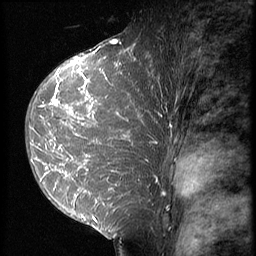
Breast MRI (dynamic contrast-enhanced), one sagittal slice; slice 39 of 64 in the series (ordered by position); 3 images stored at this slice position (order not interpretable as contrast timing); 1.5 T; TE 4.2 ms, TR 9 ms; 256 × 256 image matrix, field of view 180 × 180 mm. Female patient, age 39 years. From the clinical record (not read from this slice): setting: breast cancer imaged before/during neoadjuvant chemotherapy; receptor status: HER2-positive.
Annotated regions visible in this slice (semi-automatically segmented with operator editing):
- analysis volume of interest (the breast-tissue region the enhancement analysis was run in; not a lesion): box from (x=25, y=47) to (x=157, y=239) px
- tumour enhancement mask (voxels above the 140 % enhancement threshold inside the analysis volume of interest): (x=35, y=47)–(x=150, y=218)